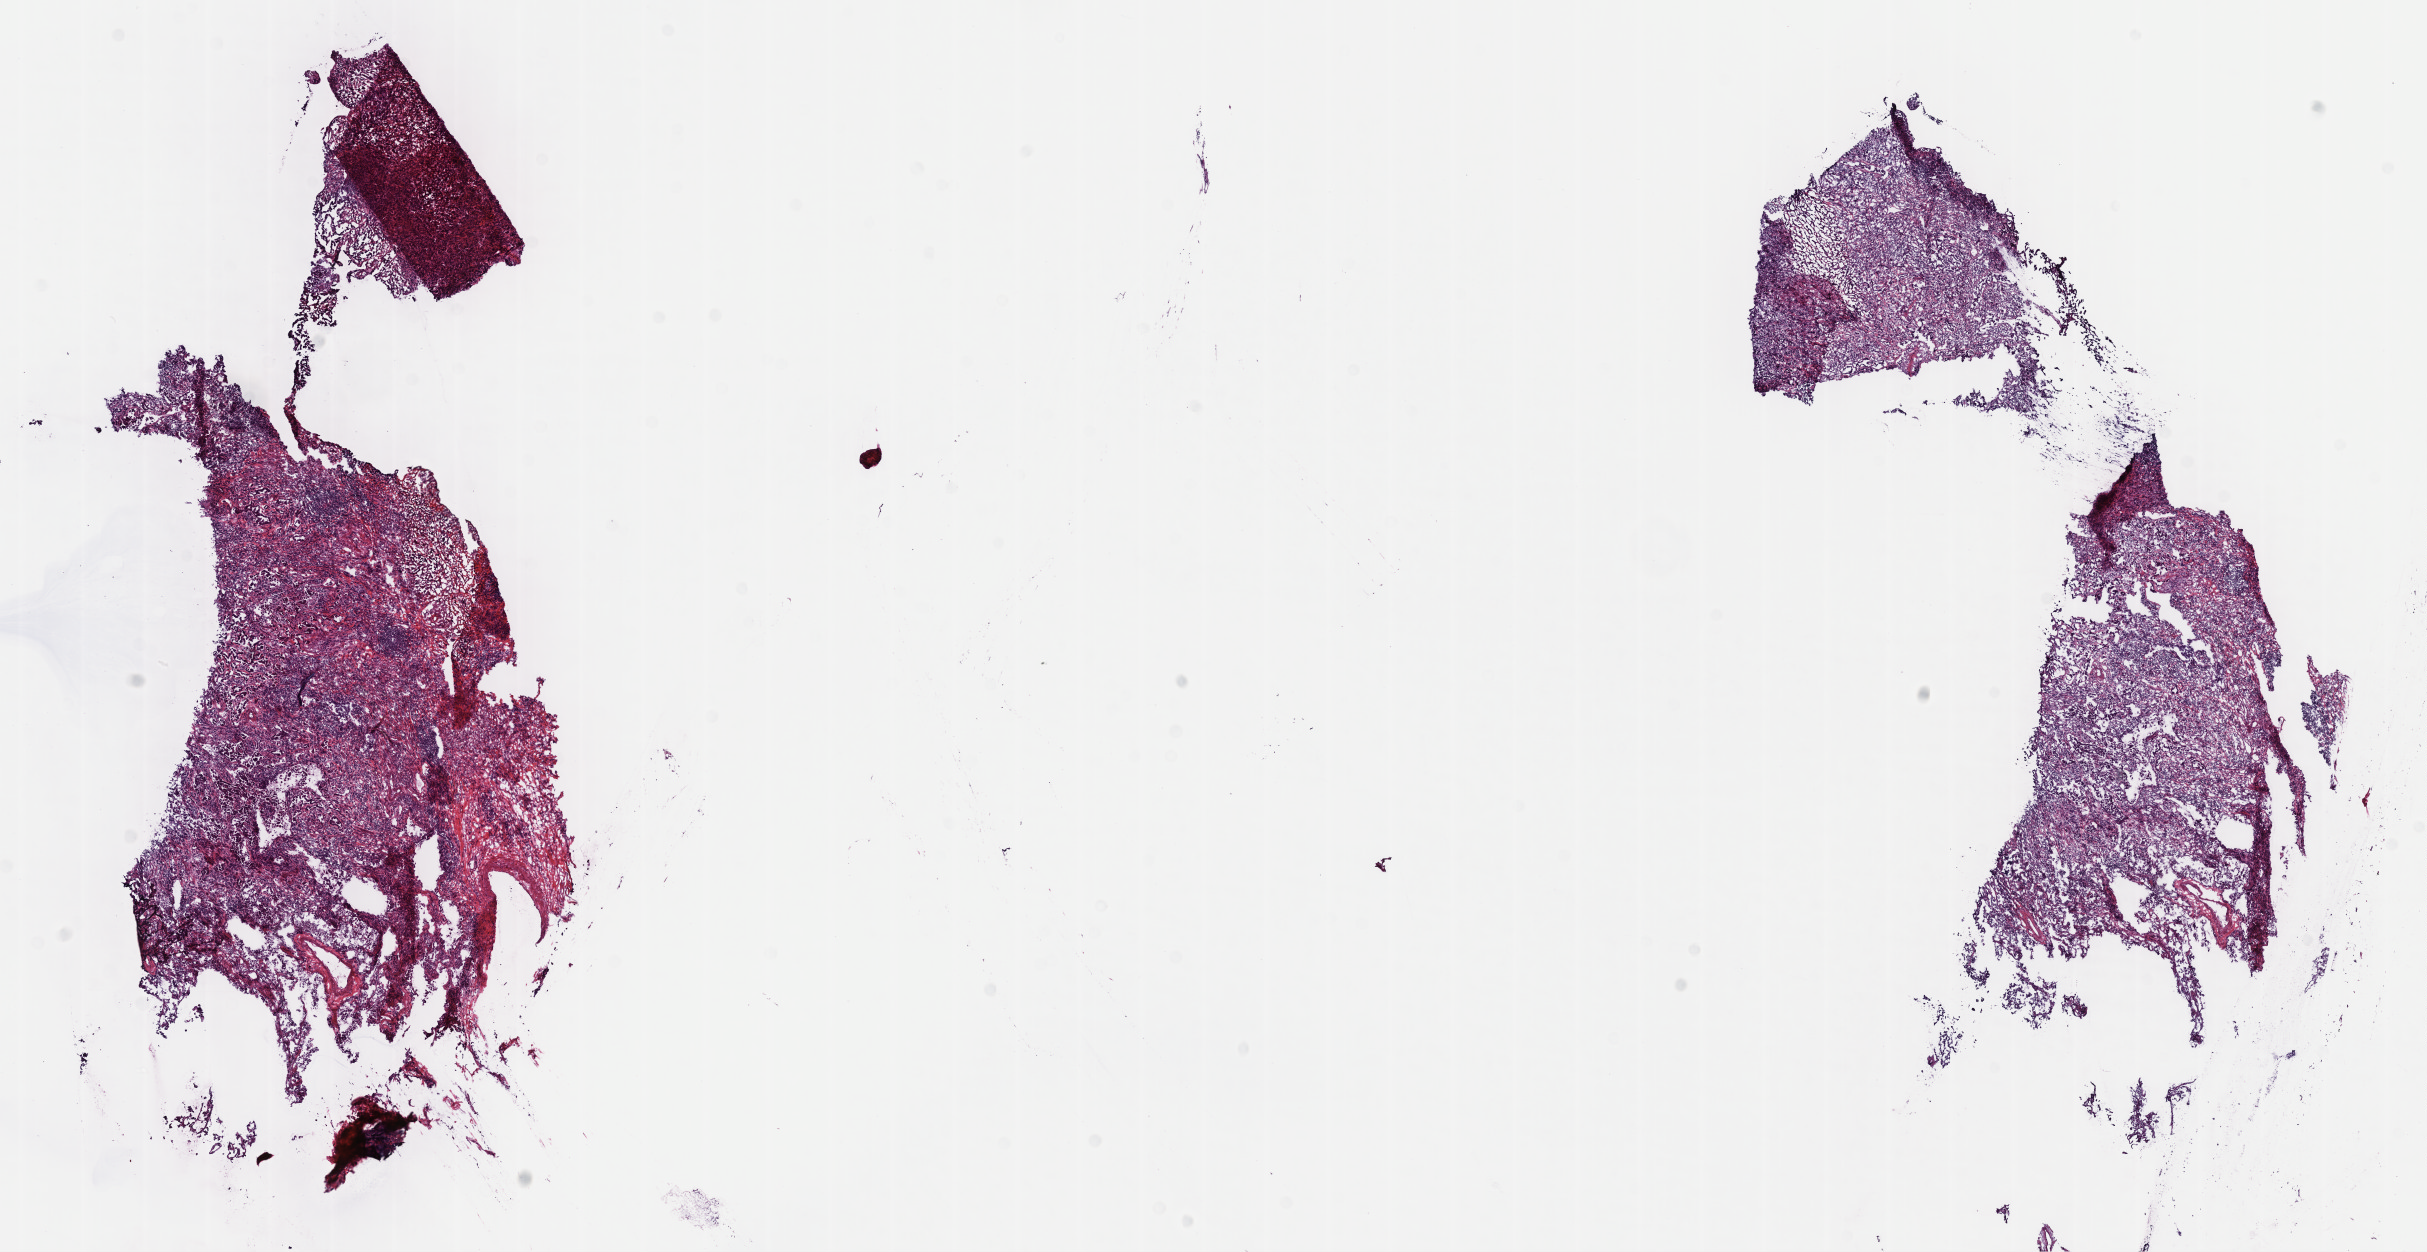
Digitized H&E tissue section (whole slide), a low-resolution overview of the entire scanned area, about 19.6 x 10.1 mm. Frozen section from the top of the tissue portion. Sample: primary tumour, lung. Female patient; age at initial diagnosis 70 years. Composition of this section per pathologist review: tumour cells 70%, tumour nuclei 70%, normal cells 0%, stromal cells 30%, necrosis 0%. Infiltration values recorded for this section: lymphocyte infiltration 40%, monocyte infiltration 20%, neutrophil infiltration 20%.
Pathologic diagnosis: Adenocarcinoma, NOS. TNM: T1a N0 M0. AJCC pathologic stage: IA.